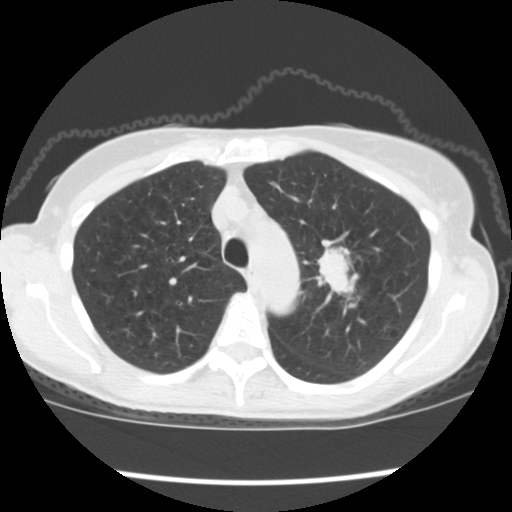
Axial slice from a low-dose chest CT screening exam, baseline screening round, lung window (W 1500 / L -600 HU), 2.5 mm slice thickness, standard (soft-tissue) reconstruction kernel (STANDARD), slice 39 of 176 in the series. Female, age 67 years at enrolment.
• Expert reader's lesion annotation, bounding box [x1, y1, x2, y2] px = [307, 234, 380, 311].
• The exam's reader record, not a measurement of the box and not confirmed to be the same lesion: non-calcified nodule or mass ≥4 mm, left upper lobe, 34 × 32 mm, spiculated (stellate) margins, soft tissue attenuation, pre-existing on the prior screen: no.
• Official screen result: positive, change unspecified: nodule(s) >= 4 mm or enlarging nodule(s), mass(es), or other non-specific abnormalities suspicious for lung cancer.
• Participant outcome: lung cancer diagnosed 17 days after this screen — small cell carcinoma, NOS, left upper lobe, stage IIIA (AJCC 6th edition), 40 mm at pathology.